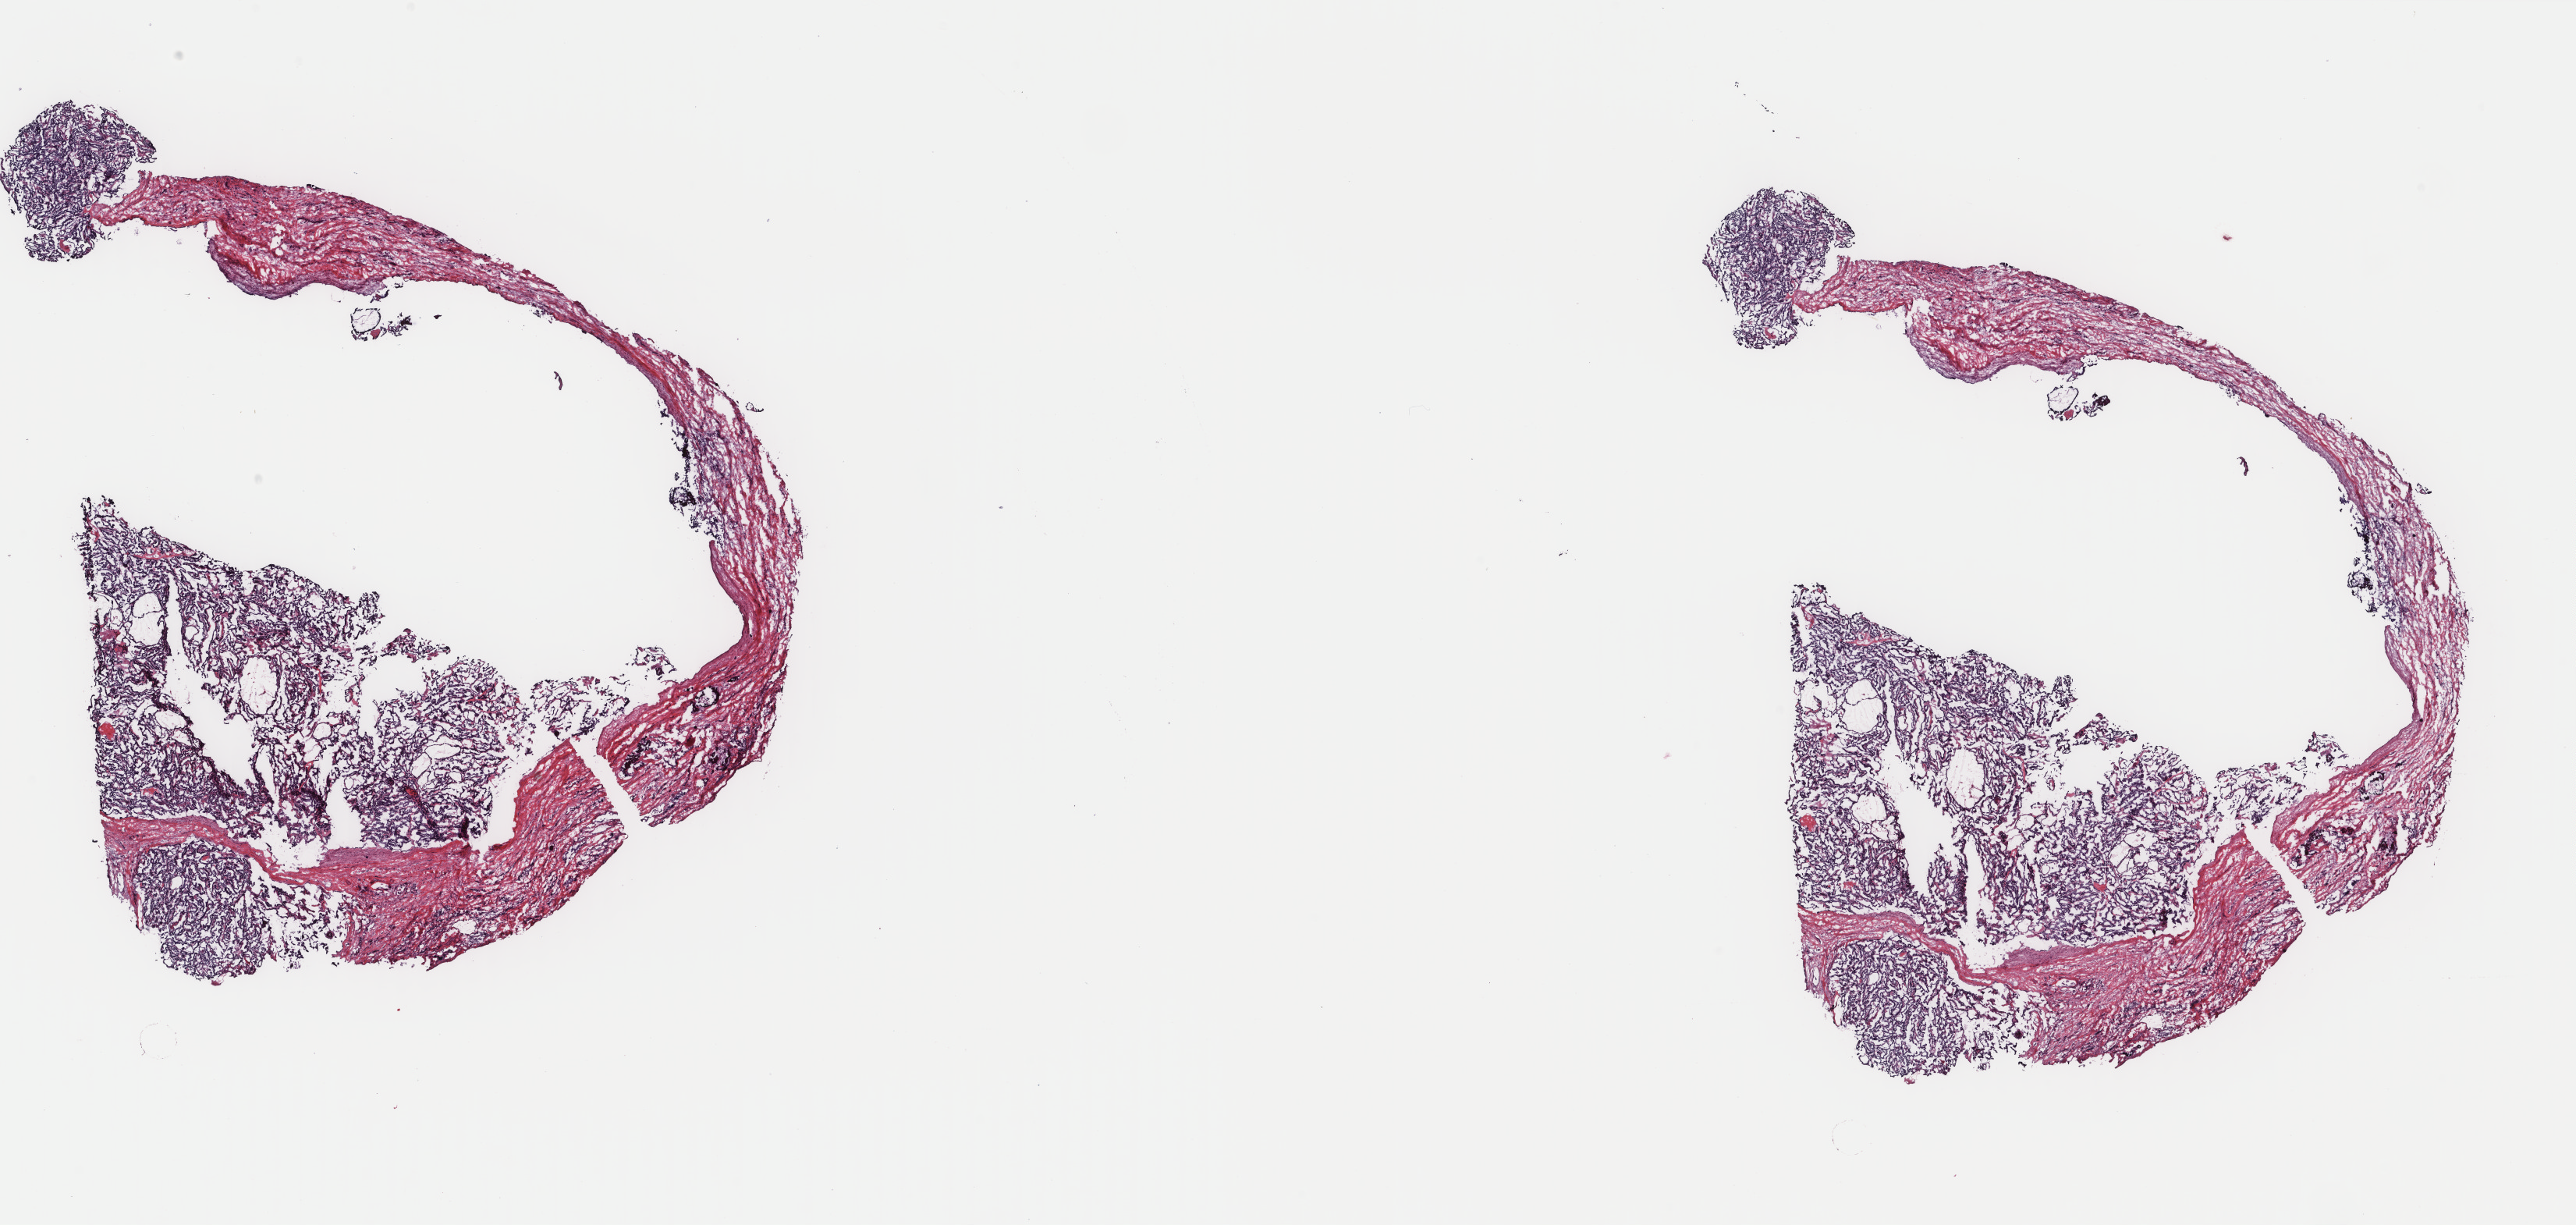
Whole-slide histology image, H&E-stained, whole scanned area (about 26.2 x 12.5 mm, acquisition: 40x scan) shown as a low-resolution overview, frozen section, thyroid, primary tumour sample. Female, age 34 years at initial diagnosis. Slide review estimates, as recorded: tumour cells 50%, tumour nuclei 60%, normal cells 0%, stromal cells 40%, necrosis 10%. Infiltration values recorded for this section: lymphocyte infiltration 2%, monocyte infiltration 0%, neutrophil infiltration 0%.
• AJCC pathologic stage: I (6th edition)
• diagnosis: Papillary adenocarcinoma, NOS